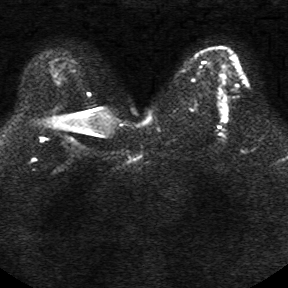
Breast MRI, one axial slice; position 20 of 34 along the scan axis; diffusion-weighted series; image 2 of 4 stored at this slice position (different b-values; order by instance number); 1.5 T; 5 mm slice thickness; 288 × 288 image matrix, field of view 340 × 340 mm. Female patient.
Outlined on this slice (manually delineated by an expert):
- tumour on diffusion-weighted imaging: bounding box <221,76,225,80> (left, top, right, bottom; pixels)